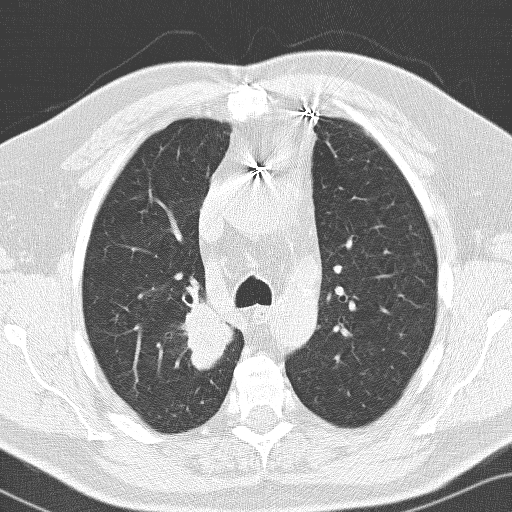
Low-dose screening chest CT, one axial slice; position 104 of 141 along the scan axis; lung window (W 1500 / L -600 HU); 3.2 mm slice thickness; 512 × 512 image matrix.
Structures marked on this image (outlined manually by an expert reader):
- lesion 1 (tumor, upper lobe of right lung): bounding box [x1, y1, x2, y2] px = [181, 301, 233, 370]